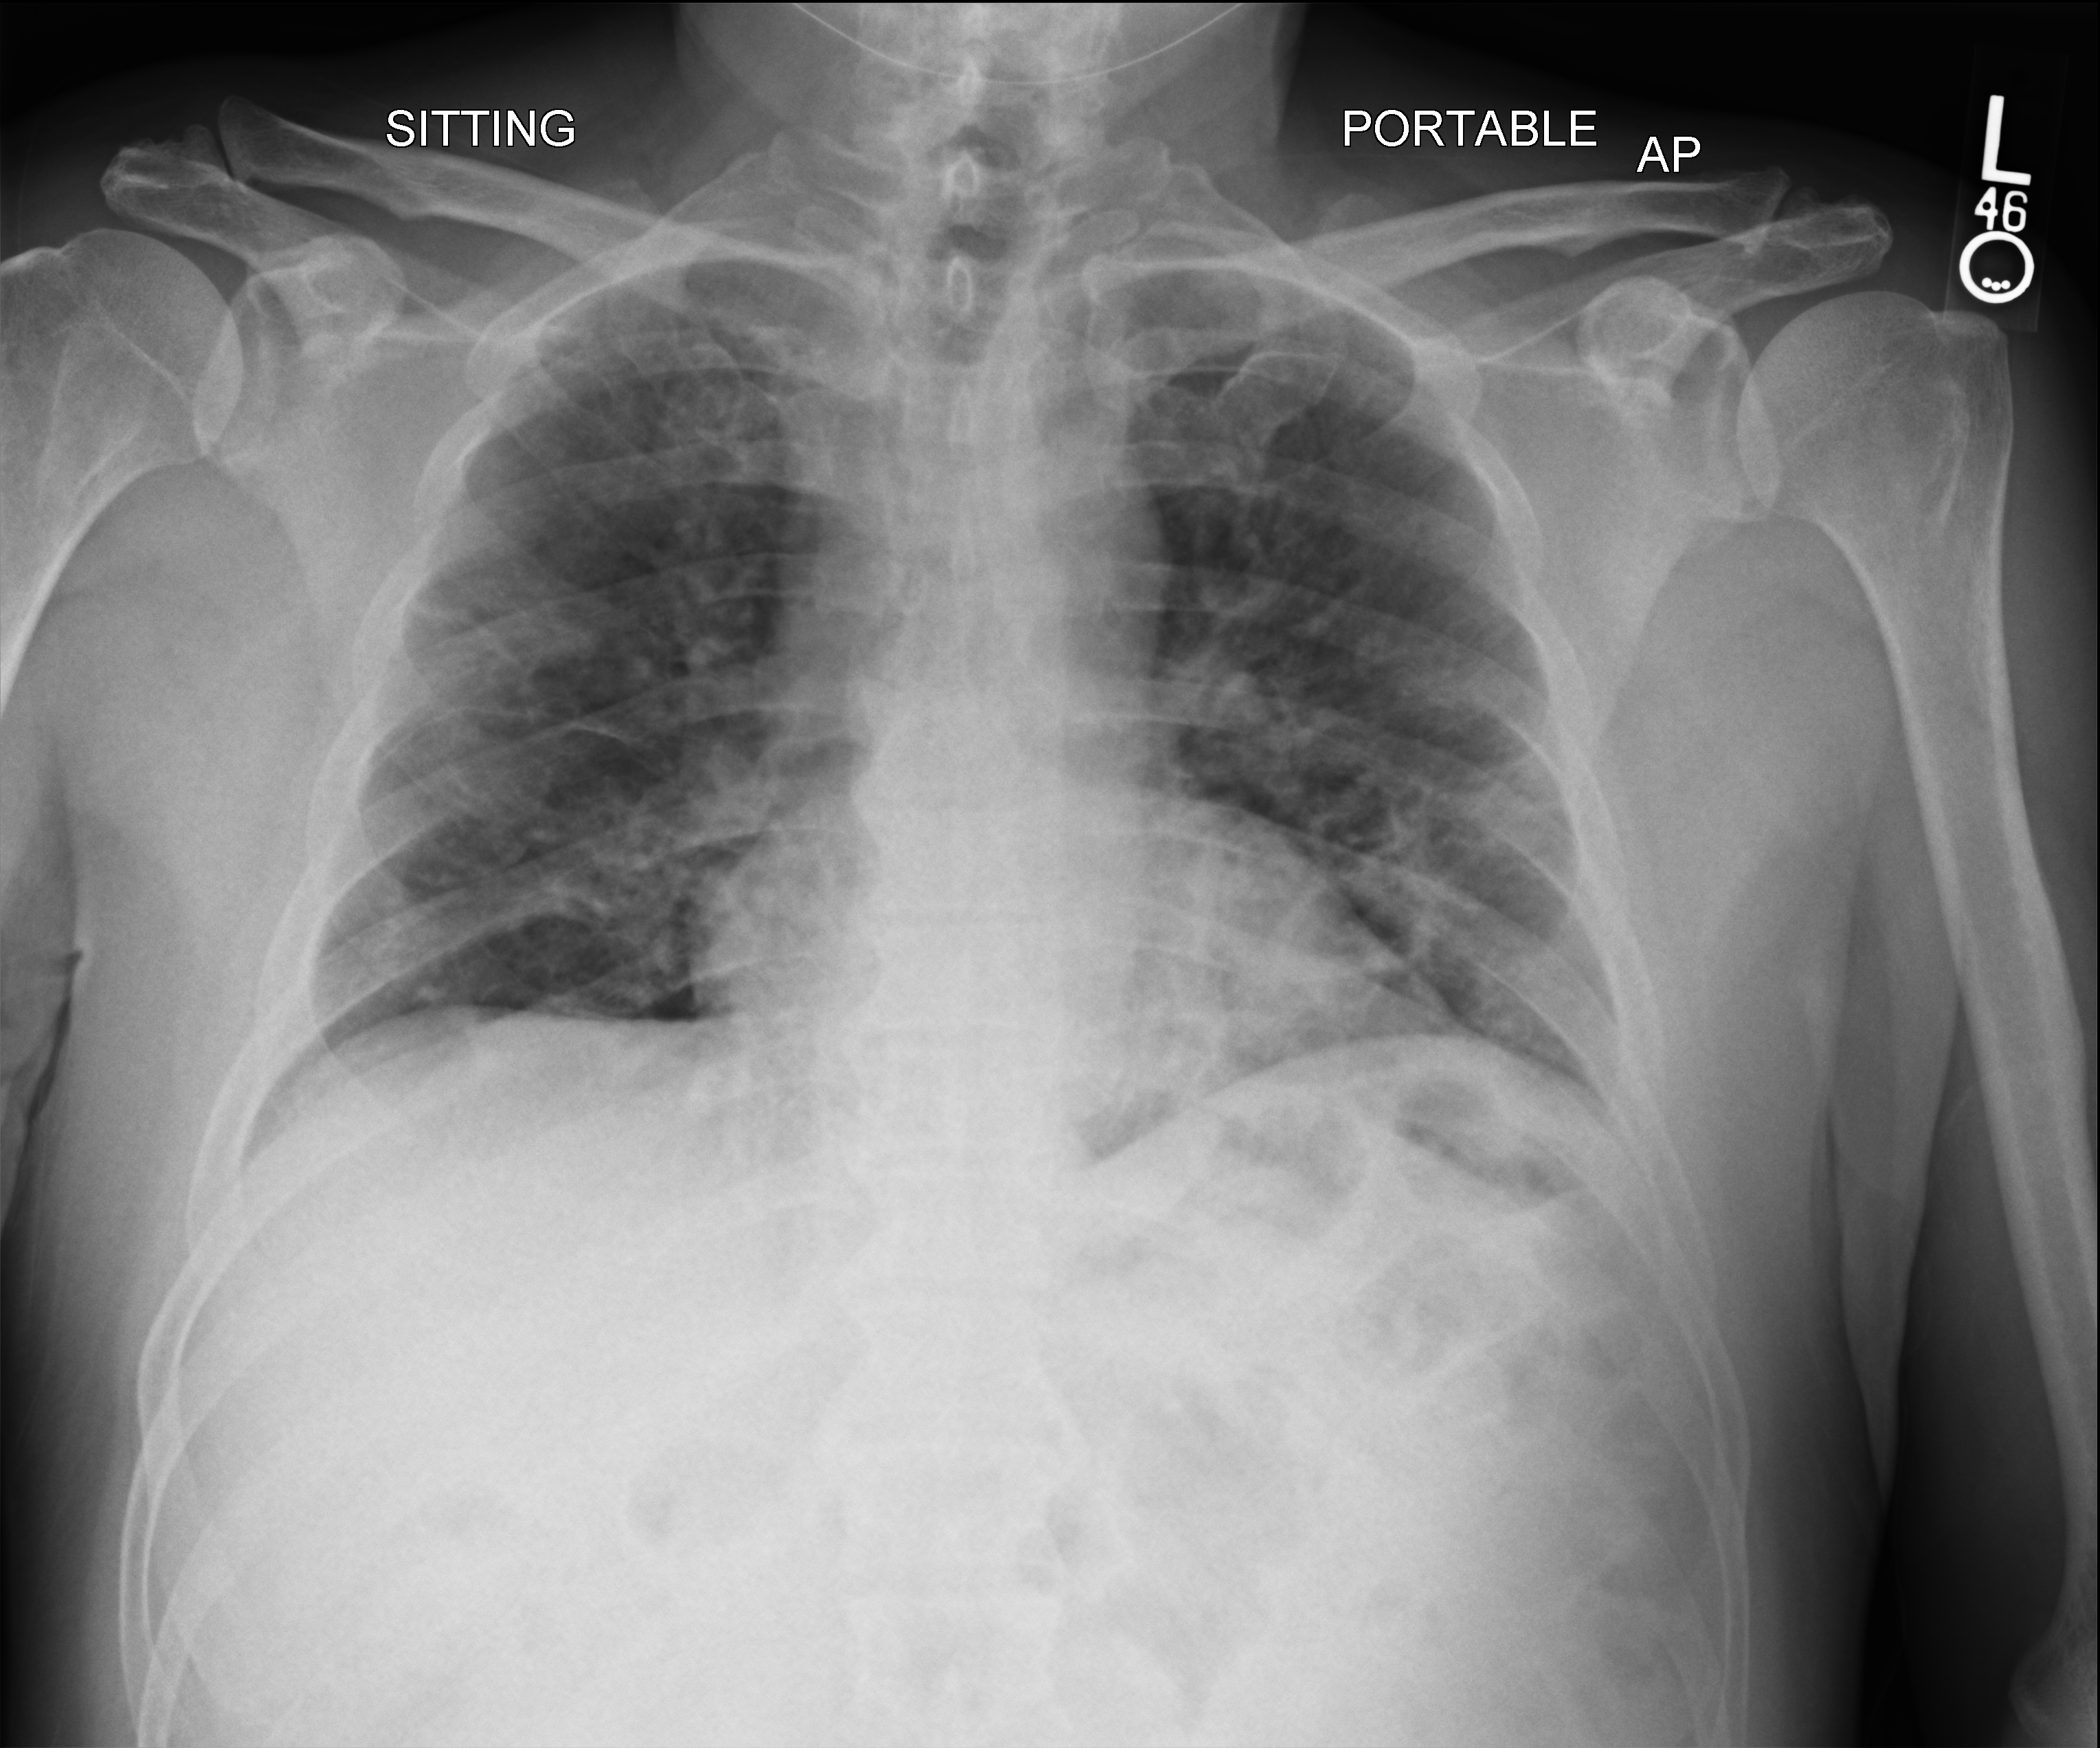
Portable chest radiograph. Male patient hospitalised with COVID-19, age 60–74 years.
From the hospital-stay record, not from the radiograph (when in the stay this image was taken is not recorded): diabetes (admission record): no; mechanically ventilated during this hospital stay: no.